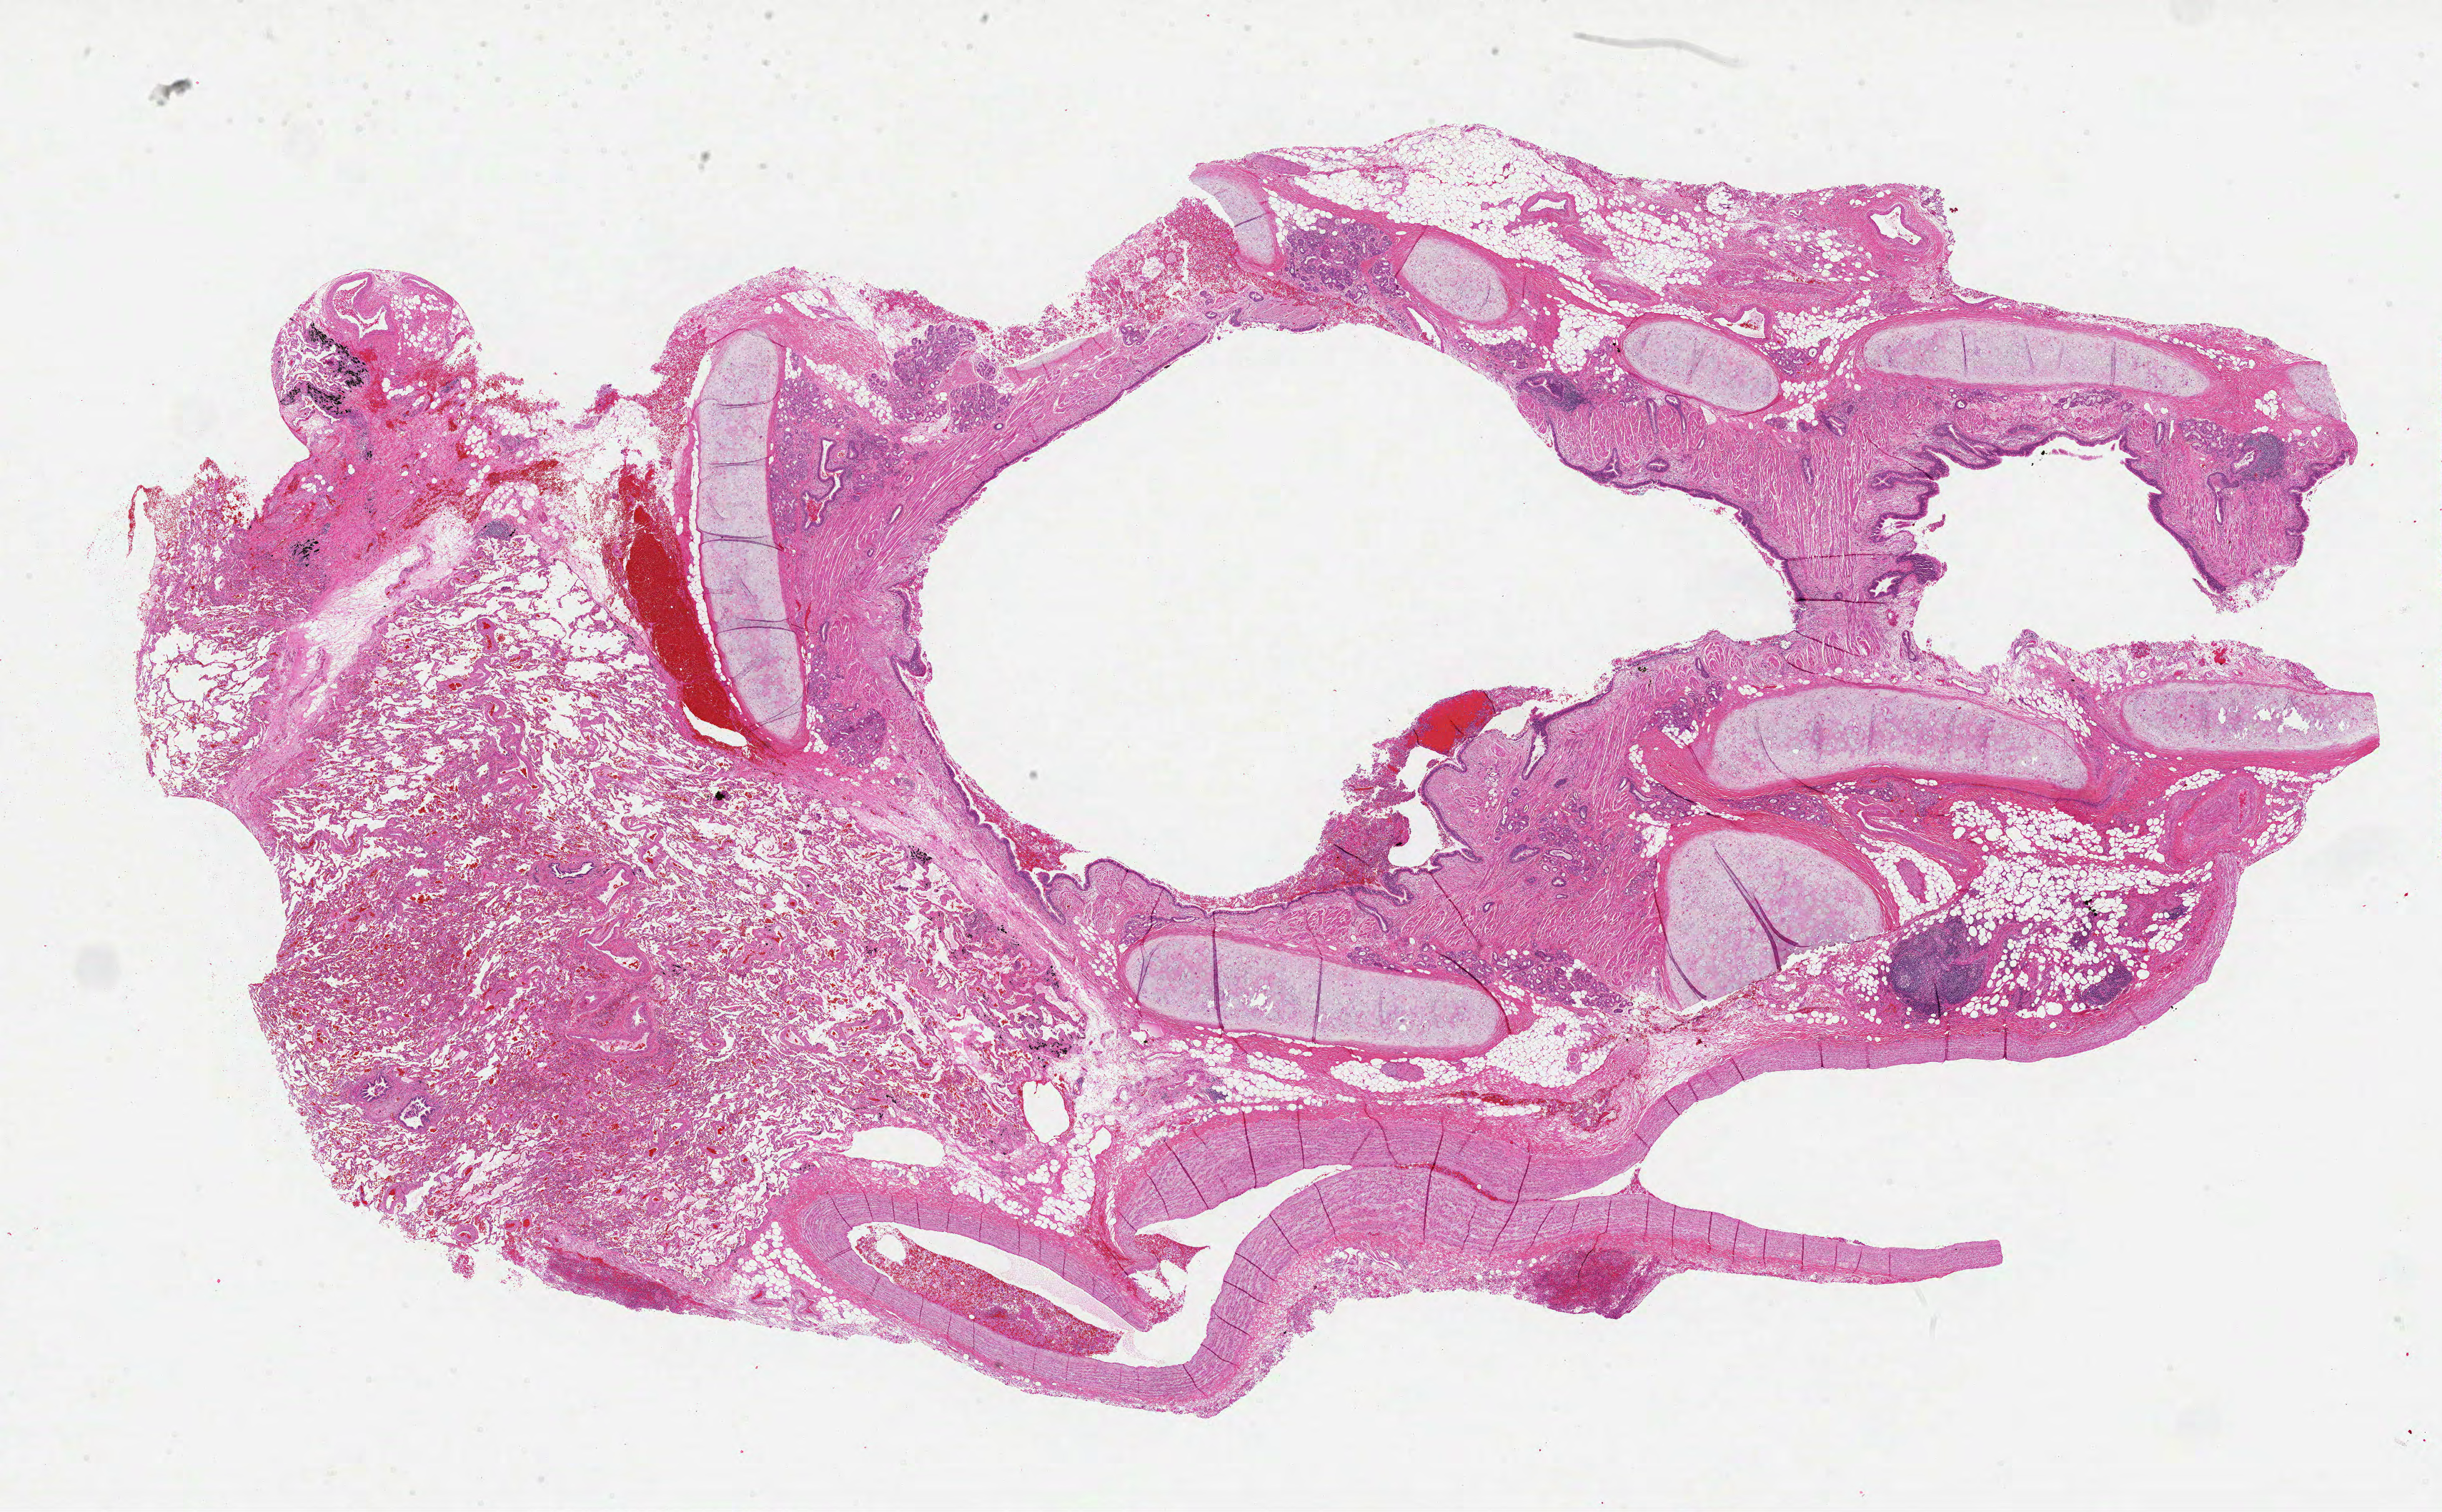
Digitized Hematoxylin and eosin (H&E) stained tissue section (whole slide), shown as a low-resolution overview of the whole scanned area (about 27.6 x 17.1 mm, slide scanned at 40x), formalin-fixed paraffin-embedded (FFPE) diagnostic section, sample: primary tumour, lung. Male, age 73 years at initial diagnosis.
- TNM: T1 N0 M0
- histologic diagnosis: Squamous cell carcinoma, NOS (lower lobe, lung)
- AJCC pathologic stage: IA (5th edition)